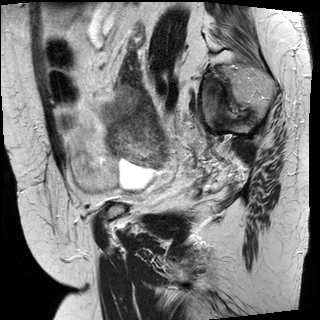
Pelvic MRI for cervical cancer, one sagittal slice. Slice 24 of 30 in the series (ordered by position). T2-weighted. 1.5 T. TE 89 ms, TR 3810 ms. 4 mm slice thickness. 320 × 320 image matrix, field of view 260 × 260 mm. Female patient, age 62 years.
Structures marked on this image (outlined manually by an expert reader):
- uterus and cervix: bounding box [x1, y1, x2, y2] px = [110, 123, 165, 167]